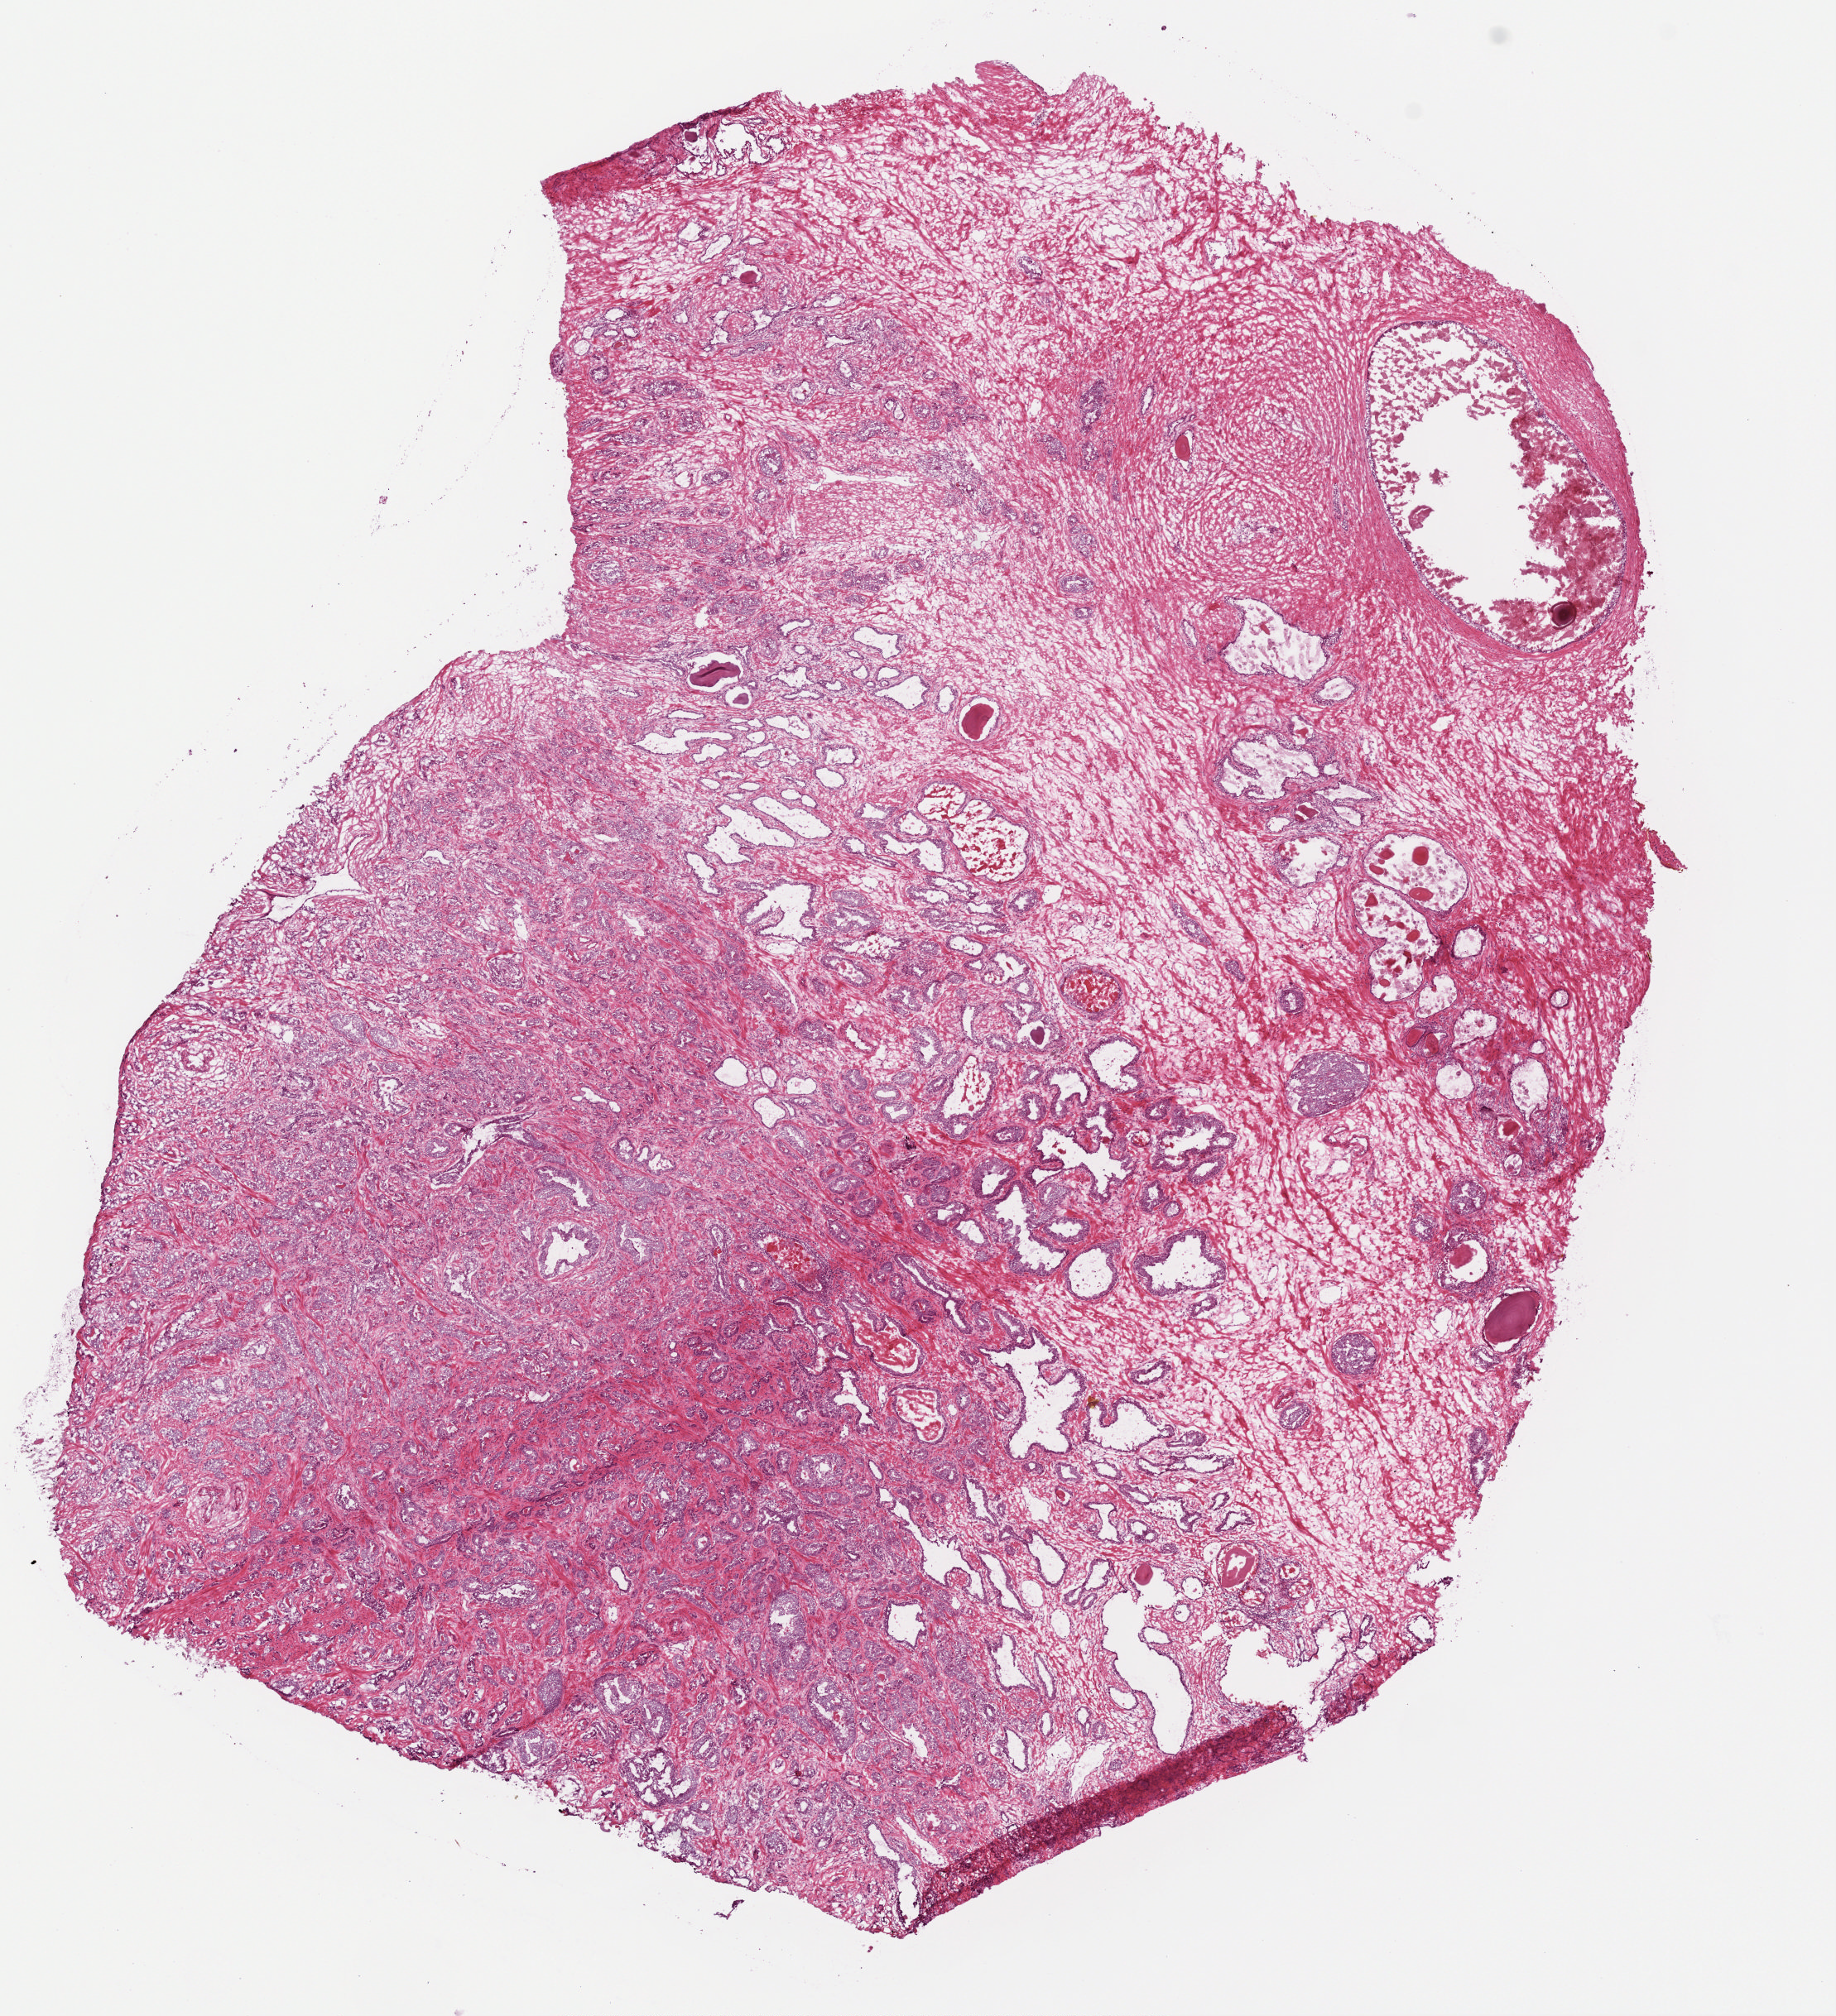
Whole-slide histology image, Hematoxylin and eosin (H&E) stained, a low-resolution overview of the entire scanned area, about 8.9 x 9.8 mm (from a 40x scan), frozen section, primary tumour sample from the prostate. Male patient; age at initial diagnosis 70 years. Pathologist review of this section (percent, as recorded): tumour cells 60%, tumour nuclei 70%.
Diagnosis: Adenocarcinoma, NOS (prostate gland).